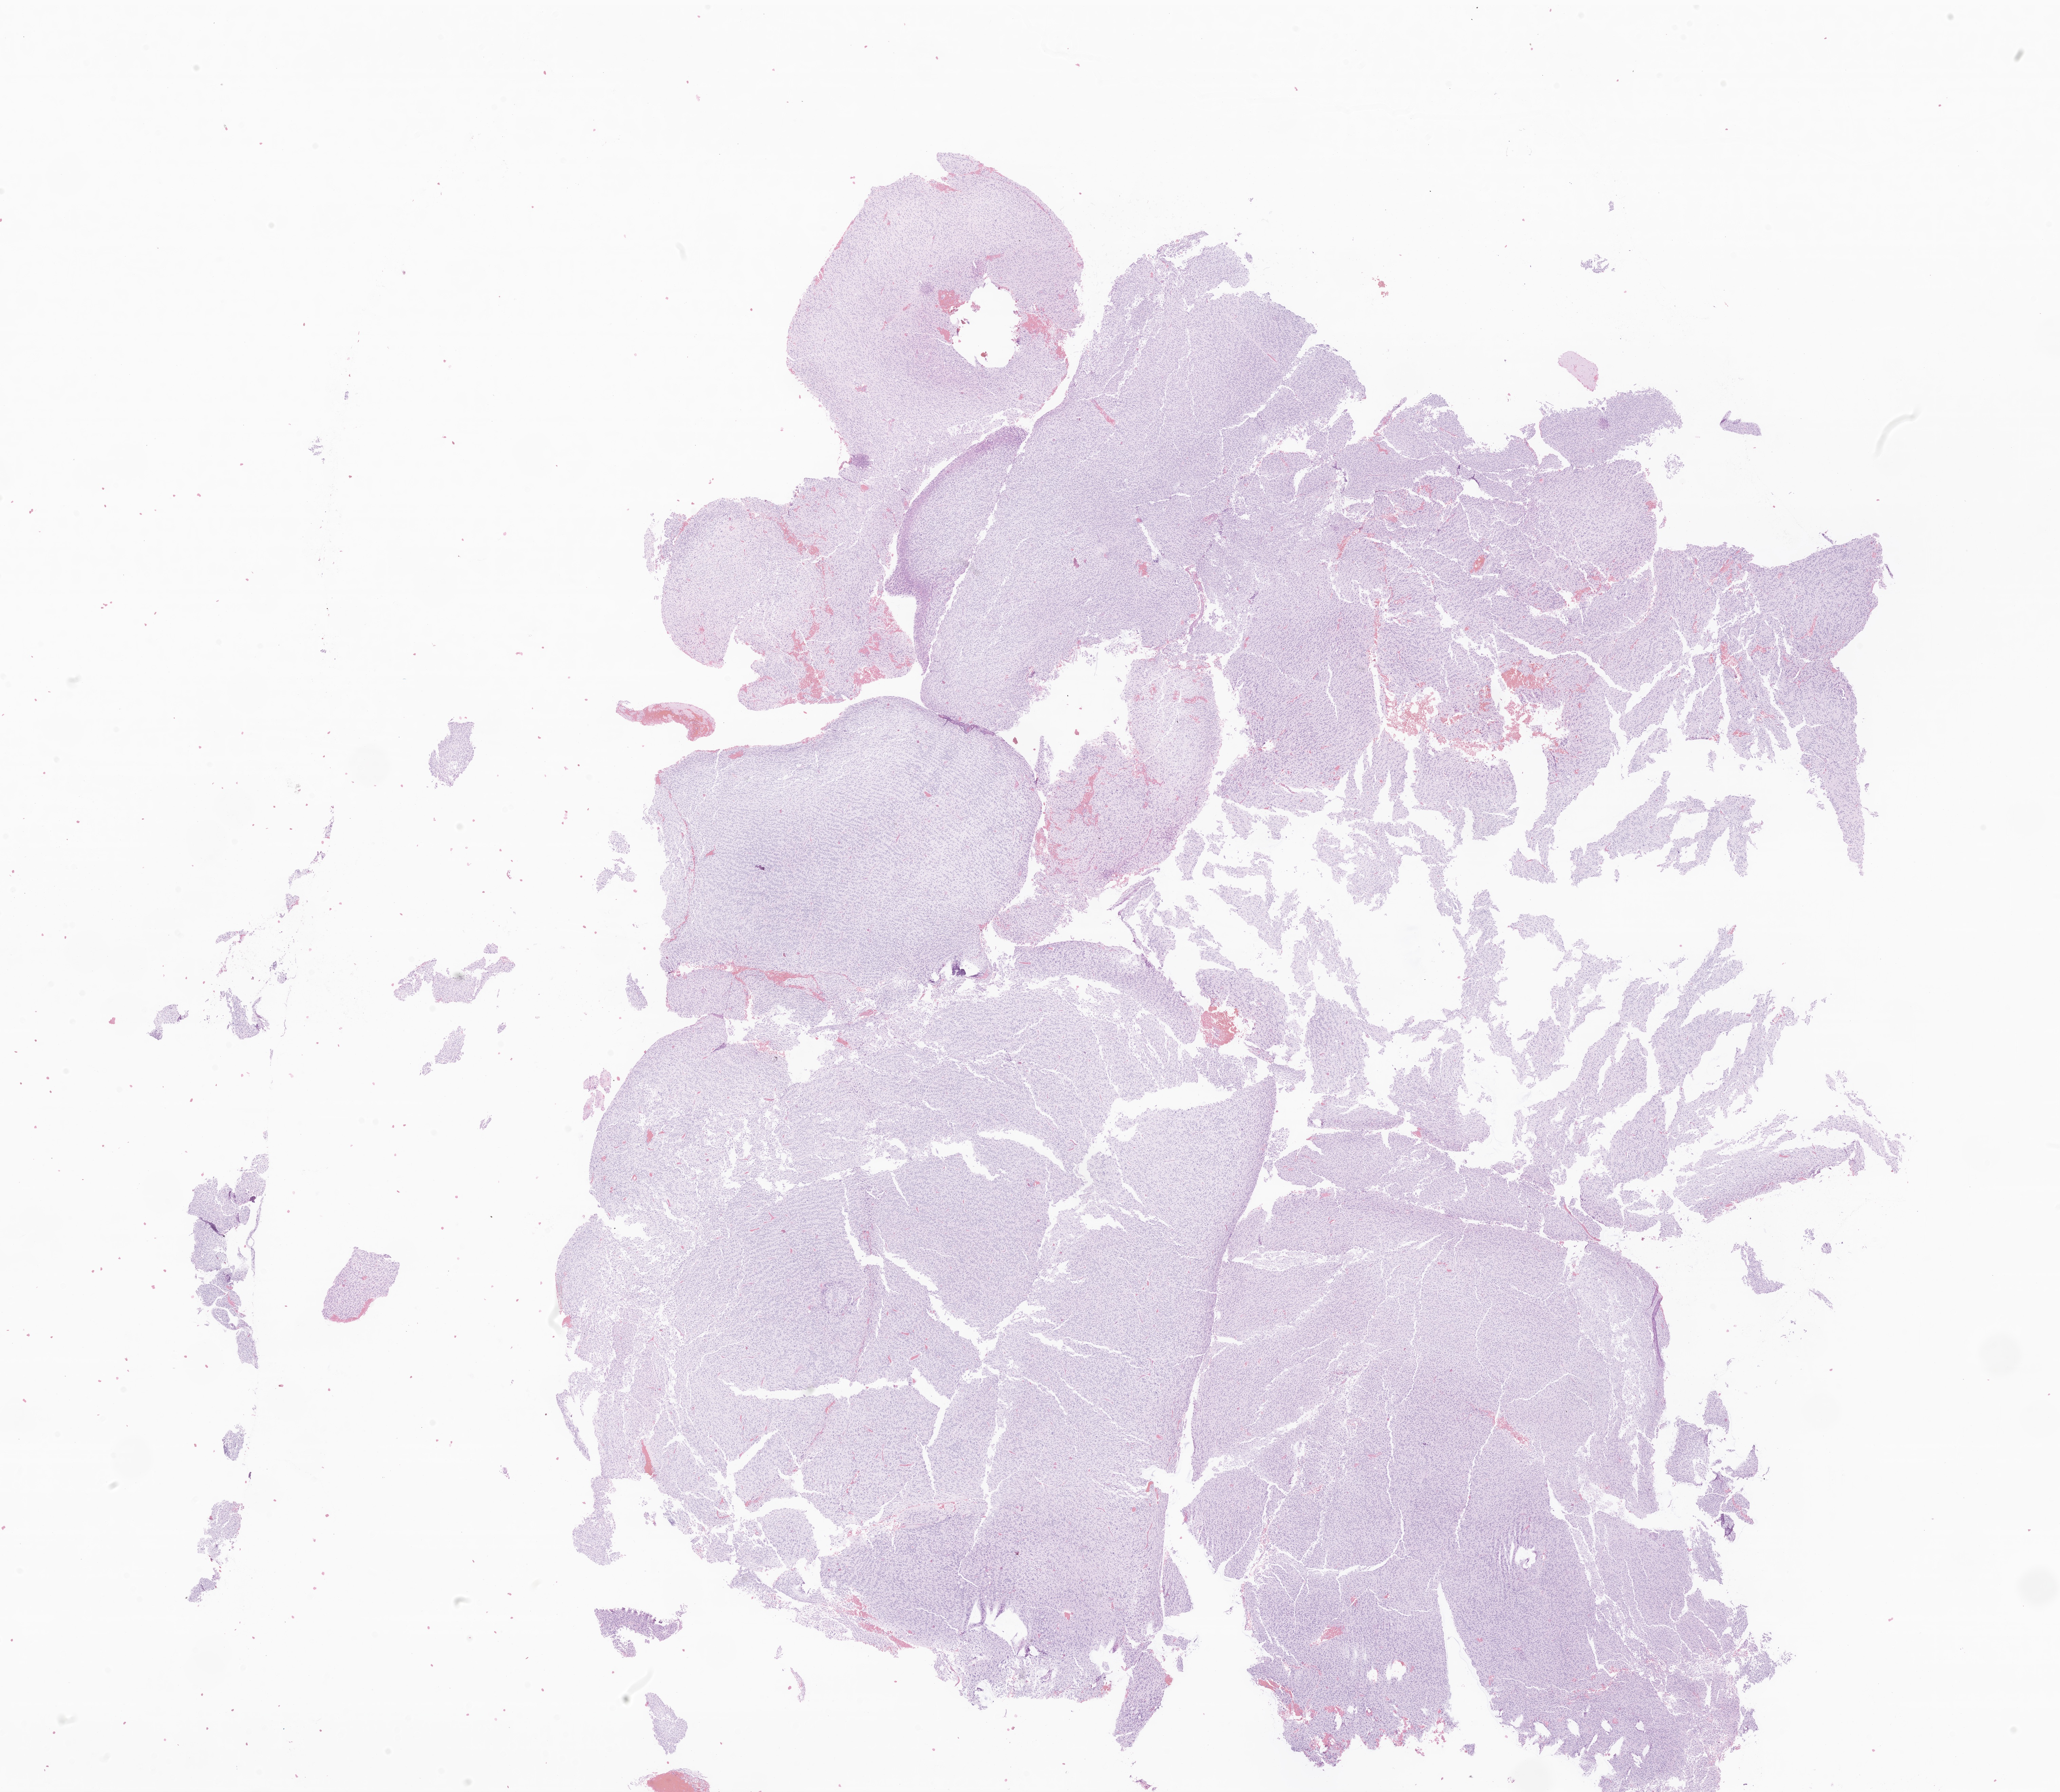
Digitized hematoxylin and eosin (H&E)-stained section of tumor tissue from the temporal lobe, a low-resolution overview of the entire scanned area, about 25.6 x 22.3 mm, formalin-fixed paraffin-embedded section. Patient: male, age 218 months.
Diagnosis (ICD-O-3 morphology term): CNS embryonal tumor, NOS.